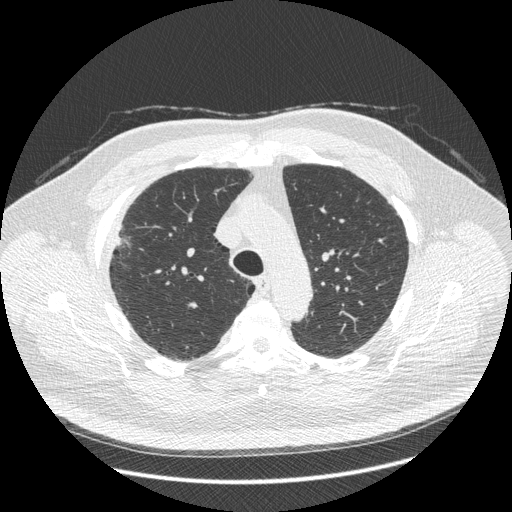
Chest CT (low-dose screening protocol), one axial image; third screening round (two years after baseline); lung window (W 1500 / L -600 HU); 1.25 mm slice thickness; 120 kVp; slice 109 of 426 in the series; 512 × 512 image matrix, field of view 400 × 400 mm. Male participant, aged 66 years at enrolment.
• Expert reader's lesion annotation, box from (x=87, y=213) to (x=149, y=272) px.
• The exam's reader record, not a measurement of the box and not confirmed to be the same lesion: non-calcified nodule or mass ≥4 mm, right upper lobe, 48 × 25 mm, spiculated (stellate) margins, soft tissue attenuation, pre-existing on the prior screen: no.
• Later outcome: lung cancer diagnosed 35 days after this screen — non-small cell carcinoma, right upper lobe, stage IV (AJCC 6th edition), 50 mm at pathology.